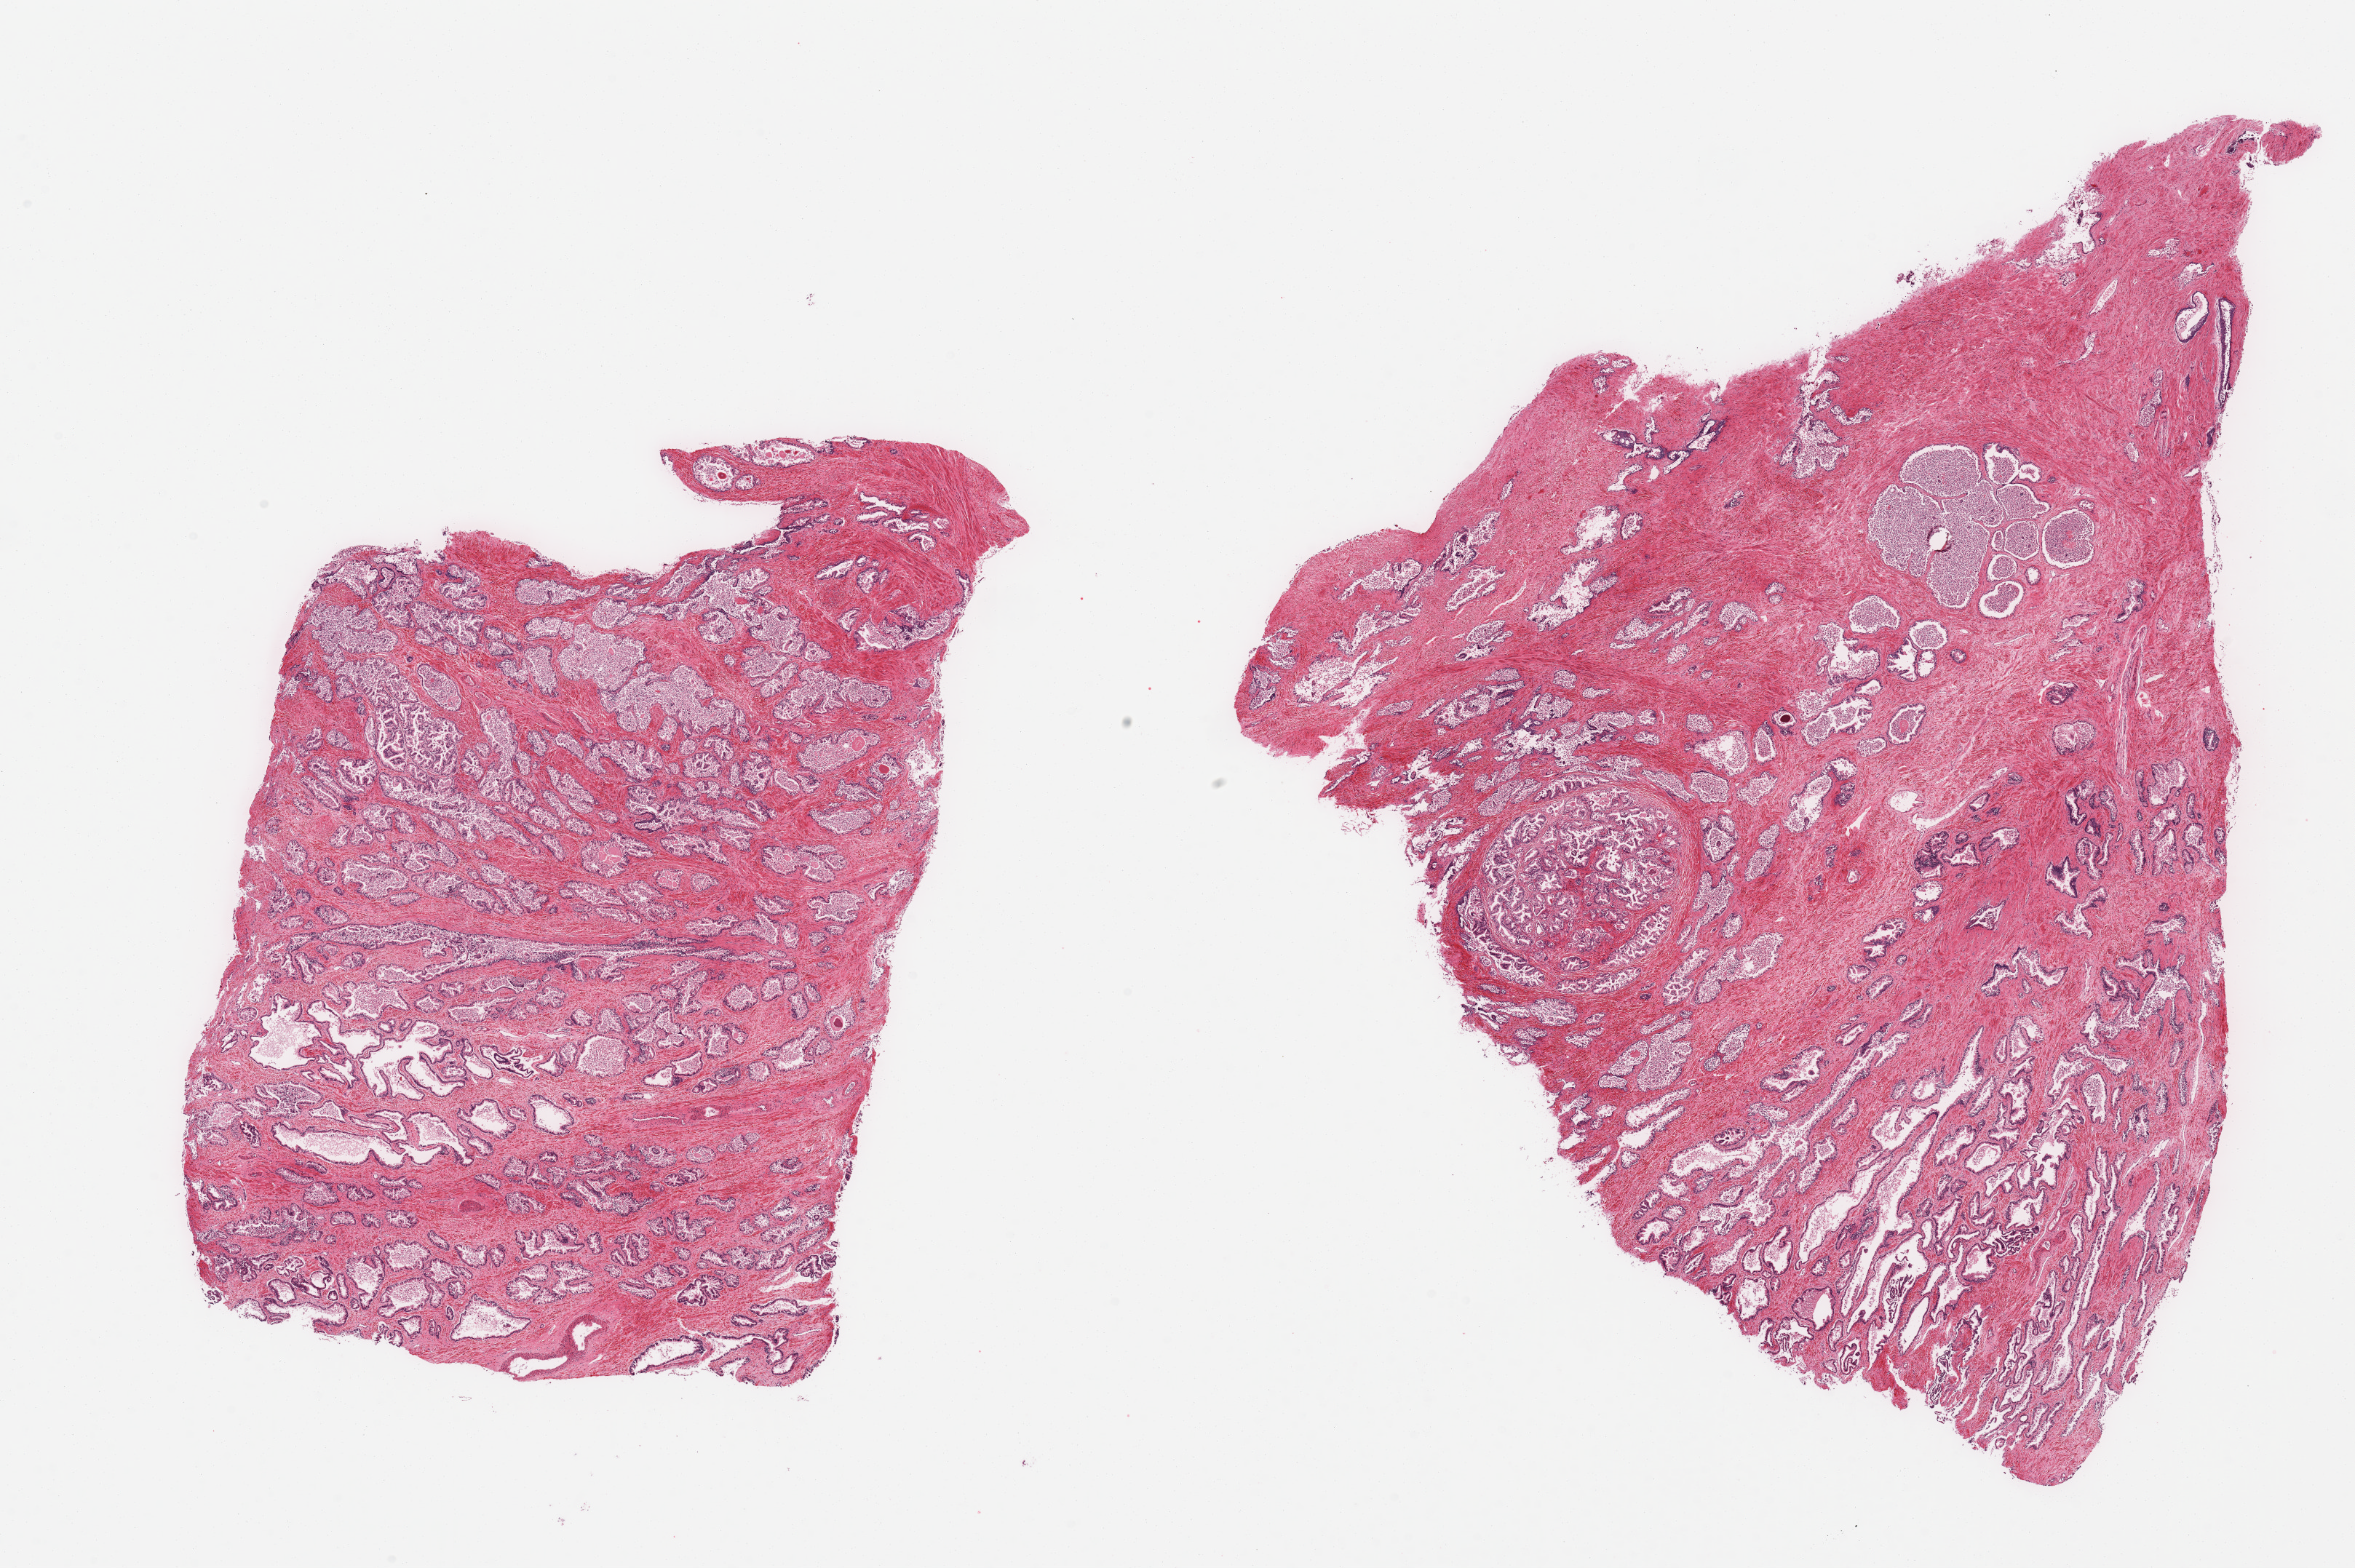
Whole-slide image, hematoxylin and eosin (H&E) stain, brightfield — whole scanned area (about 25.6 x 17.0 mm, slide scanned at 20x) shown as a low-resolution overview, PAXgene-fixed, paraffin-embedded tissue, target tissue: prostate, donor tissue sample. Donor sex: male.
Review note (as recorded): 2 pieces; fibromuscular stroma and glands with significant sloughing, nodular glandular hyperplasia.